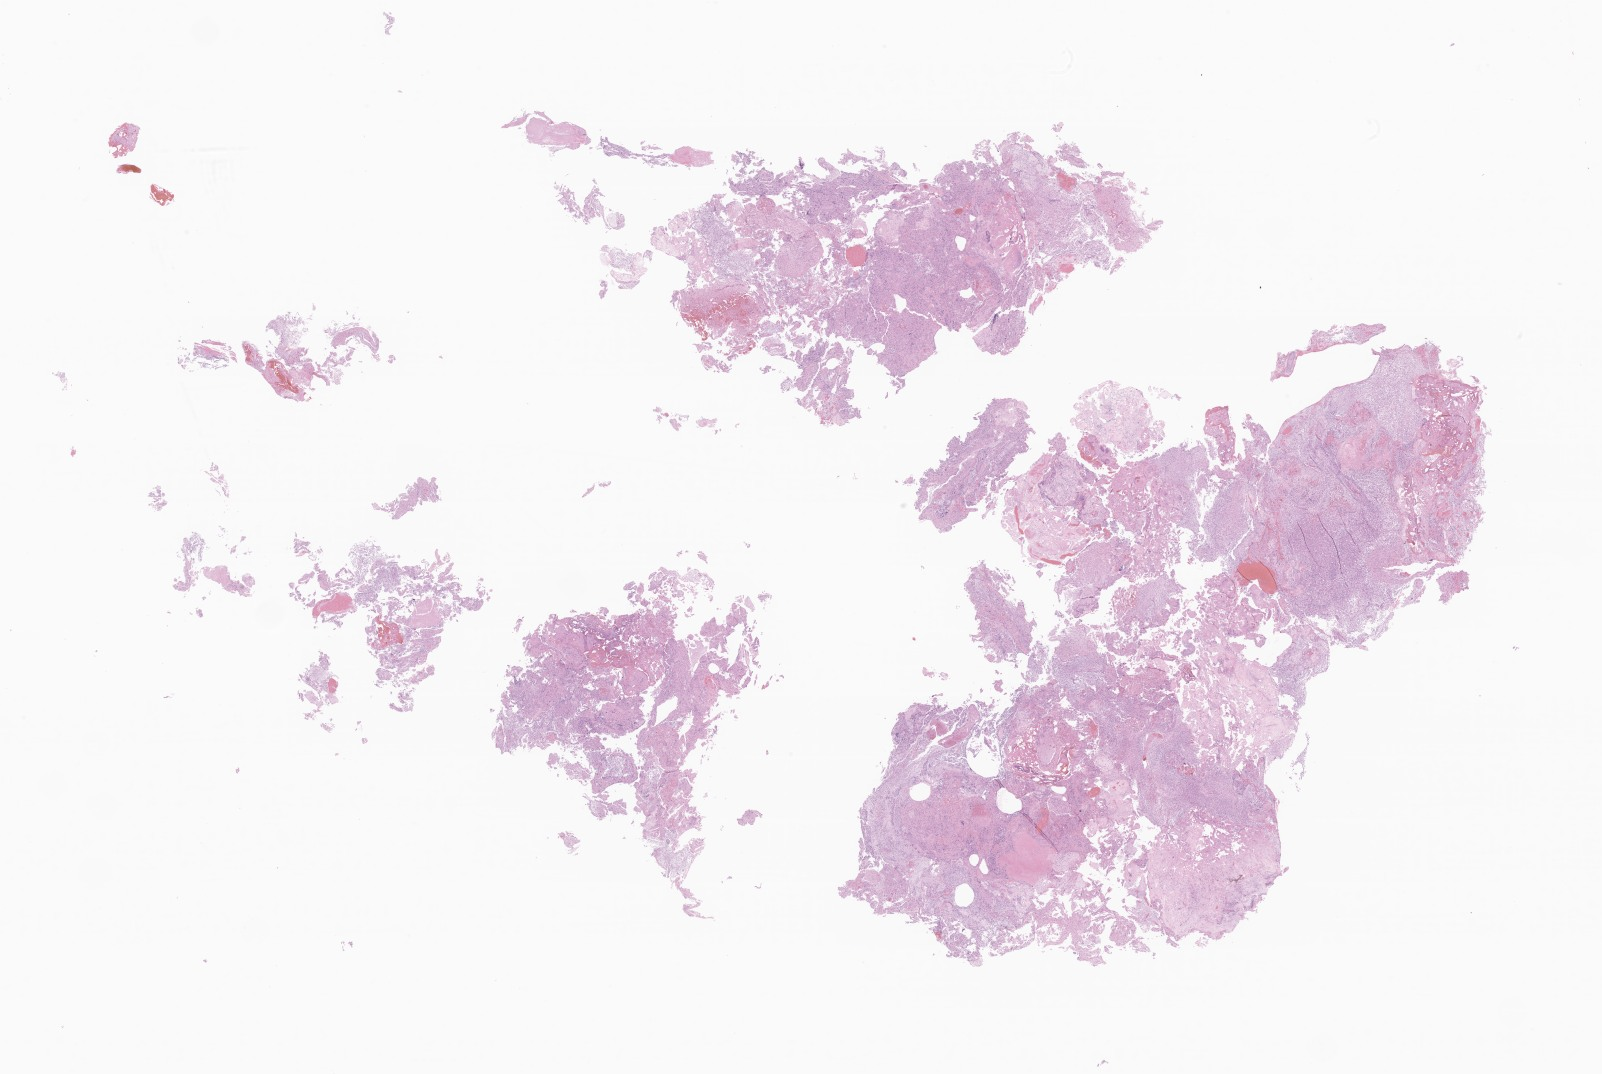
H&E whole-slide image of tumor tissue from the brain — a low-resolution overview of the entire scanned area, about 27.0 x 18.1 mm, formalin-fixed, paraffin-embedded (FFPE) tissue. Patient female; age 95 months (7 years 11 months).
Recorded diagnosis: Astrocytoma, NOS.